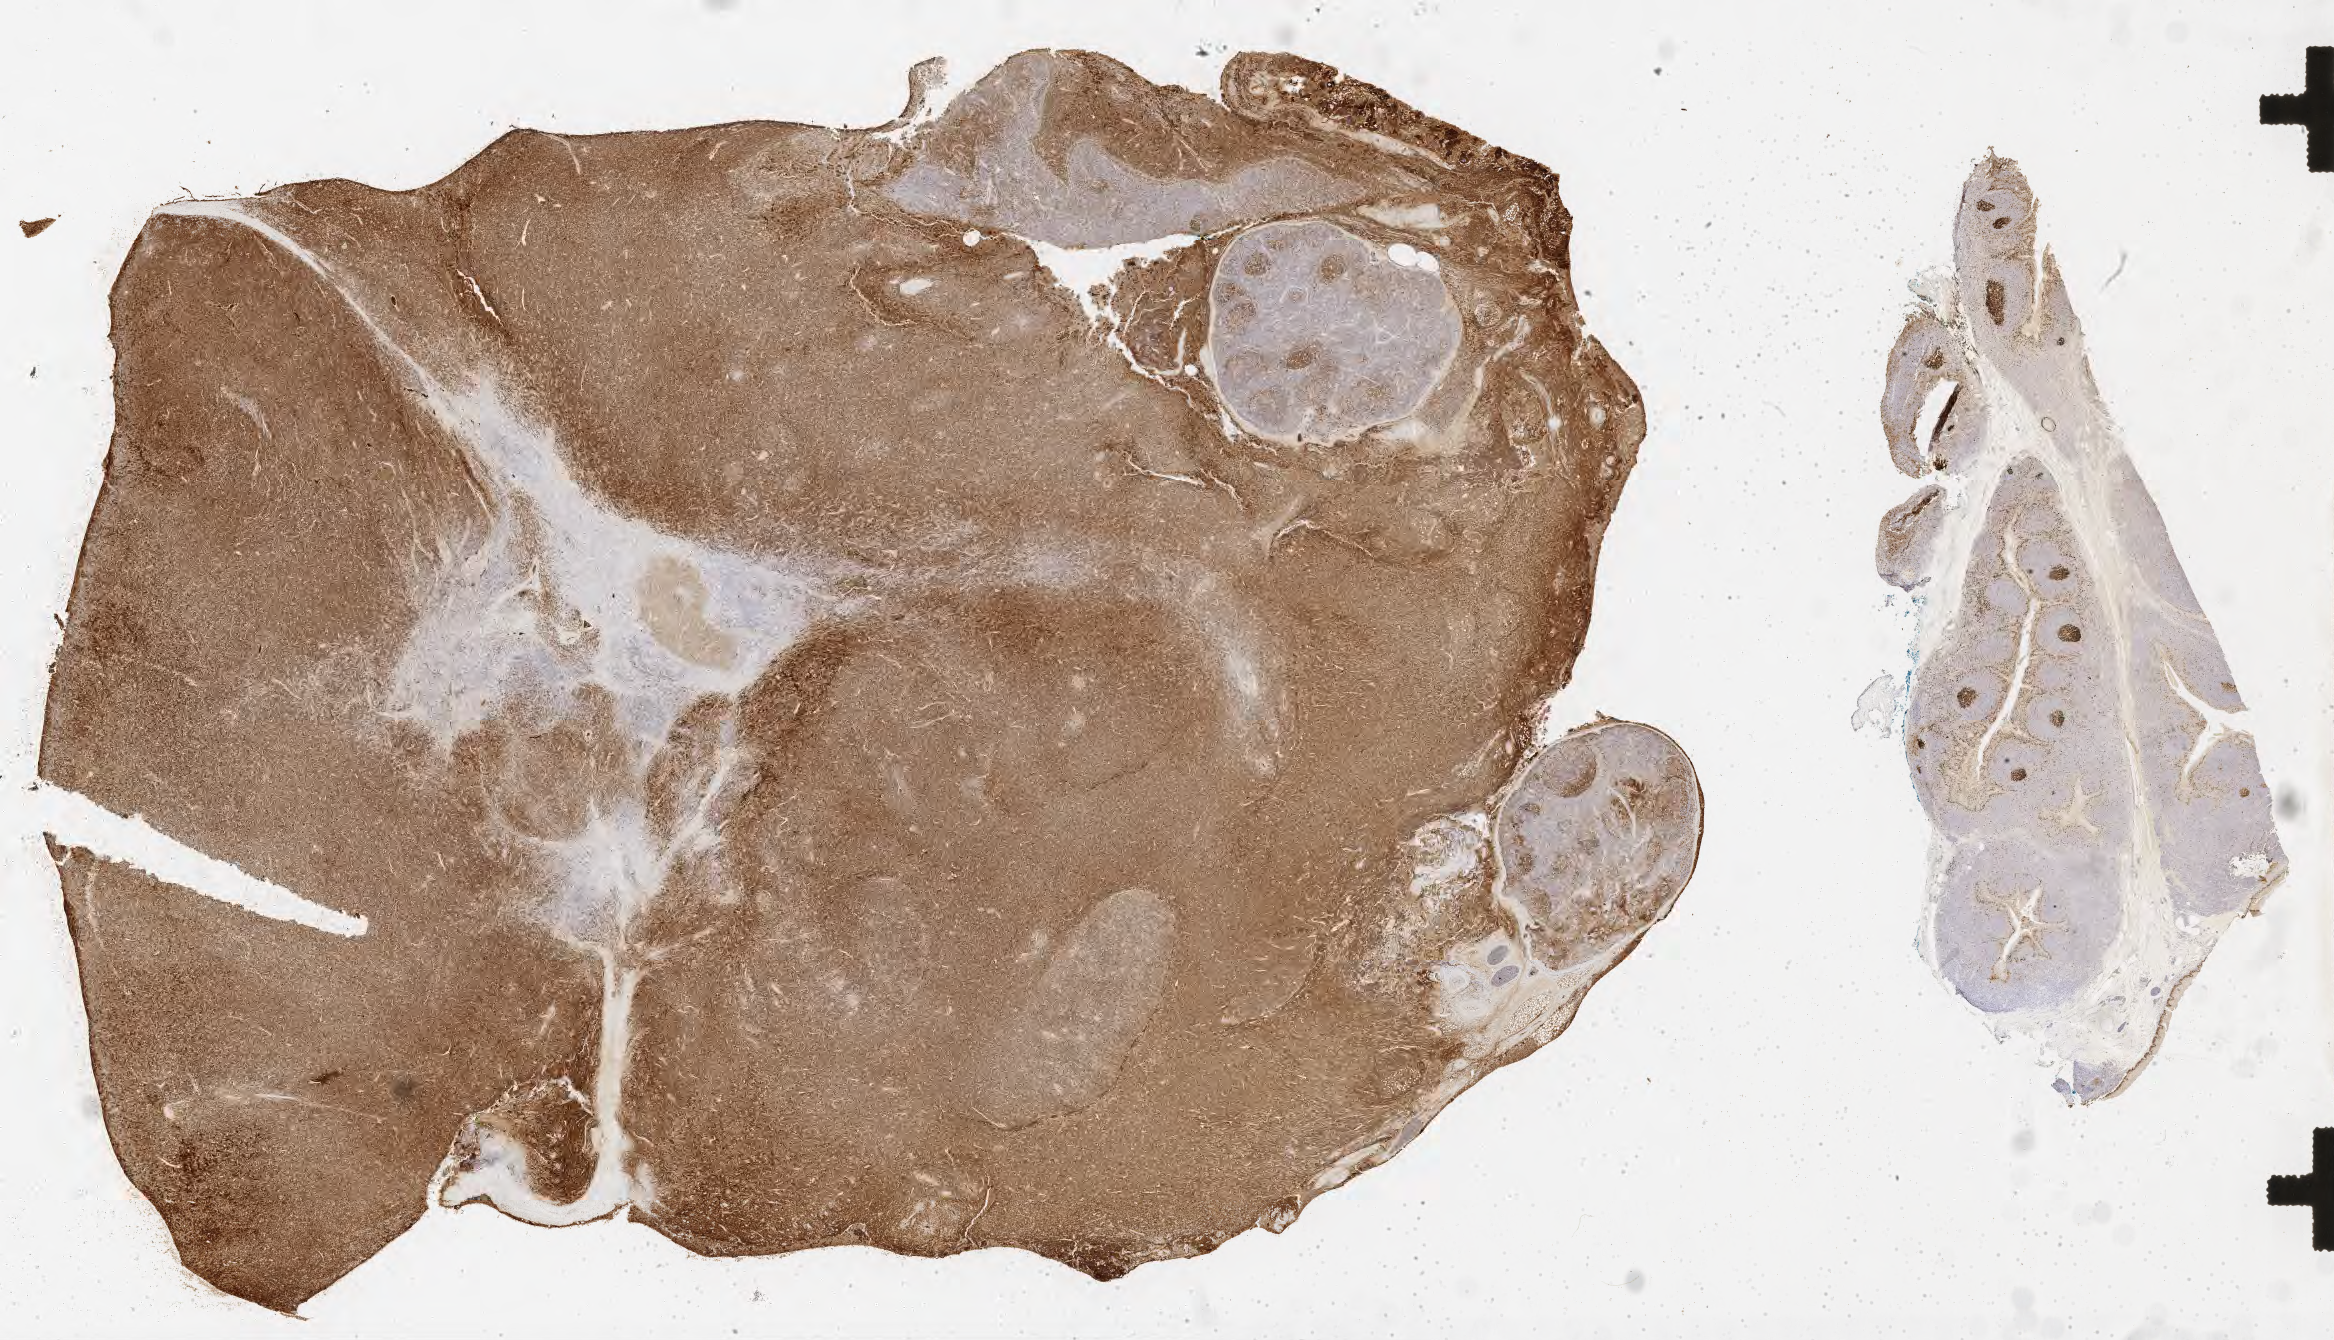
IHC for Ki-67, whole-slide image, low-resolution overview of the scanned area, about 37.7 x 21.7 mm, specimen: tumor tissue, site: lymph node of head and neck. Patient: male, age at initial diagnosis 3 years.
Histologic diagnosis: Burkitt lymphoma, NOS.